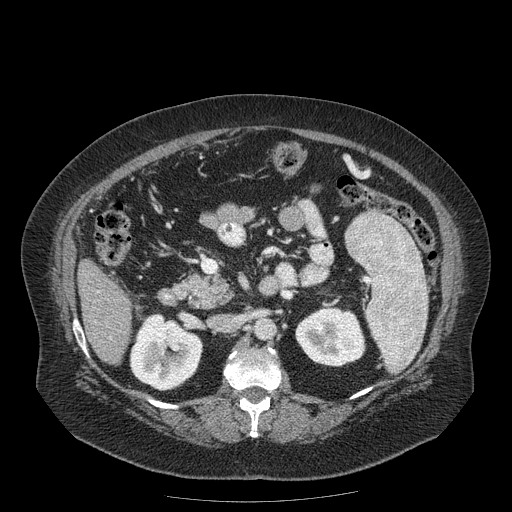
Contrast-enhanced abdominal CT (liver protocol), one axial slice. Slice 65 of 204 in the series (ordered by position). Soft-tissue window (W 400 / L 40 HU). 2.5 mm slice thickness. 512 × 512 image matrix, field of view 440 × 440 mm. From the clinical record (not read from this slice): diagnosis: hepatocellular carcinoma (patient treated with transarterial chemoembolisation; whether this scan precedes or follows treatment is not stated here); TNM stage (as recorded): Stage-IIIB; Child-Pugh class: A; tumour differentiation: well differentiated; tumour nodularity: uninodular.
Annotated regions visible in this slice (semi-automatic segmentation, software-assisted and operator-edited):
- liver parenchyma outside the tumour (the mass and vessels are separate outlines, so this box may not span the whole liver): bounding box <78,258,132,364> (left, top, right, bottom; pixels)